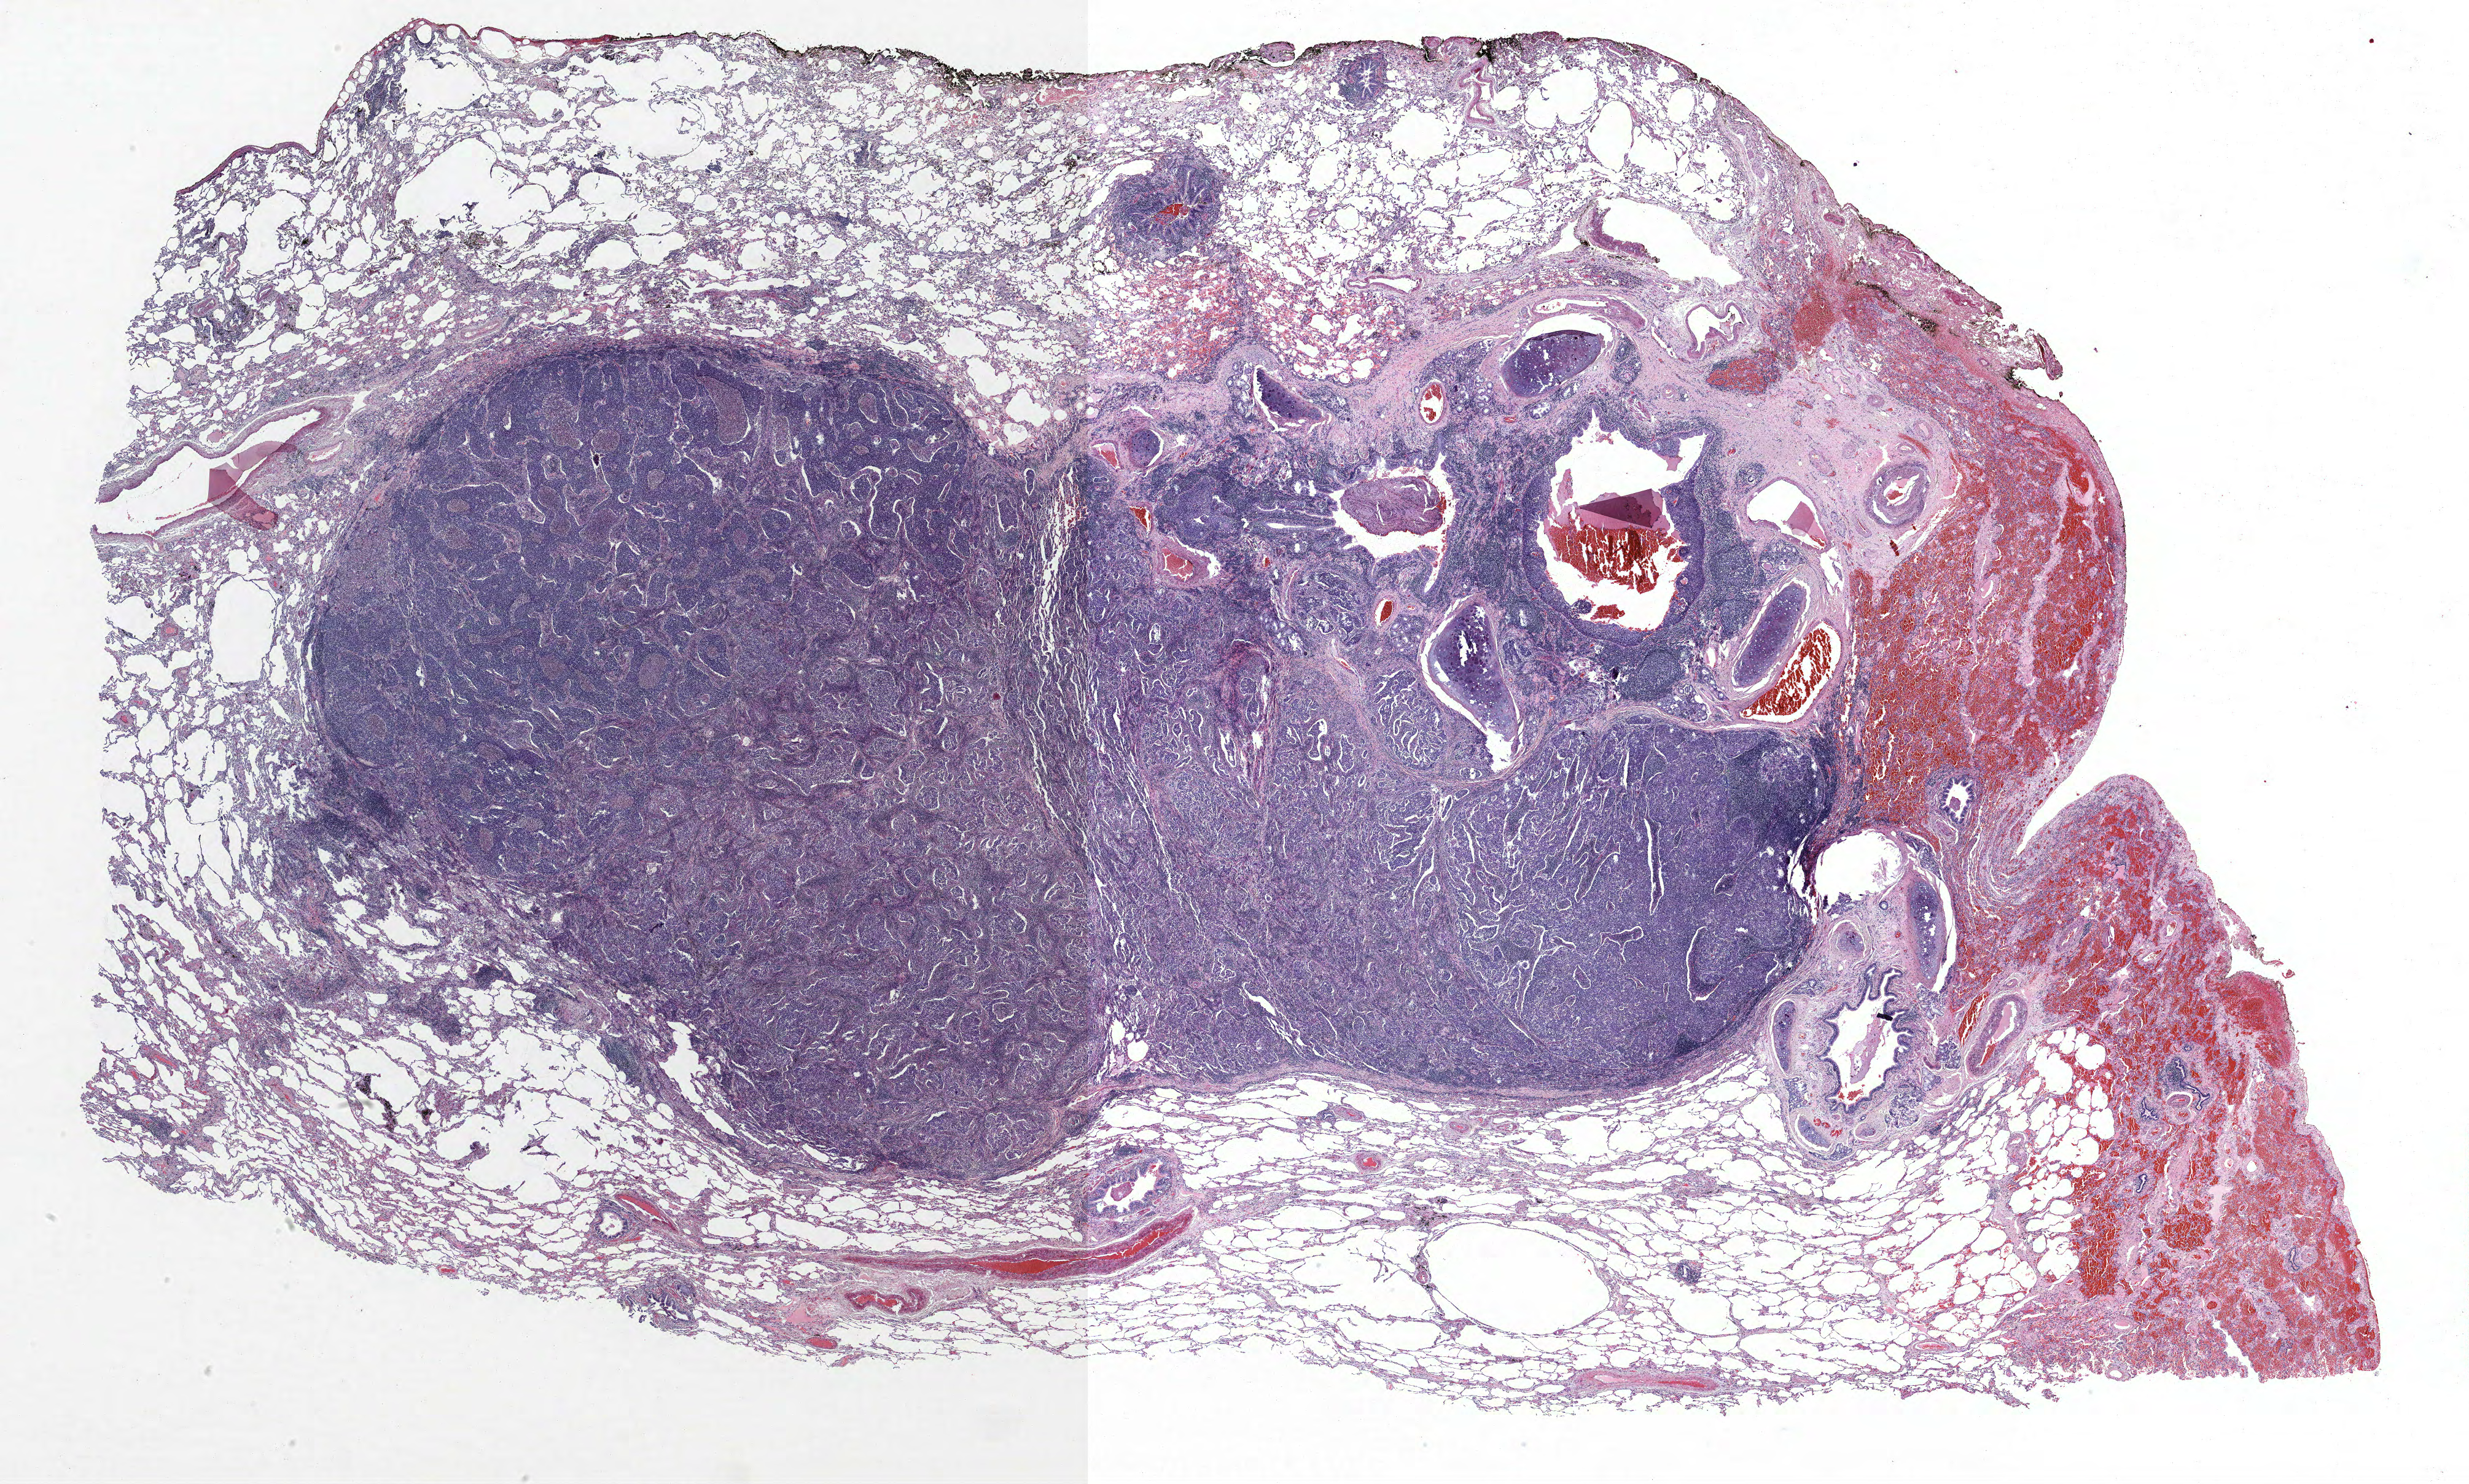
Hematoxylin and eosin (H&E) stained whole-slide image — shown as a low-resolution overview of the whole scanned area (about 32.2 x 19.3 mm); formalin-fixed paraffin-embedded (FFPE) section; lung. Female patient, aged 71 at enrolment. Former smoker at enrolment. Grade: poorly differentiated (G3).
- primary tumour location (clinical record): right upper lobe
- stage (AJCC 6th edition): IA
- tumour size (pathology): 30 mm
- ICD-O-3 topography: upper lobe of lung (C34.1)
- participant's lung-cancer diagnosis: Squamous cell carcinoma, NOS